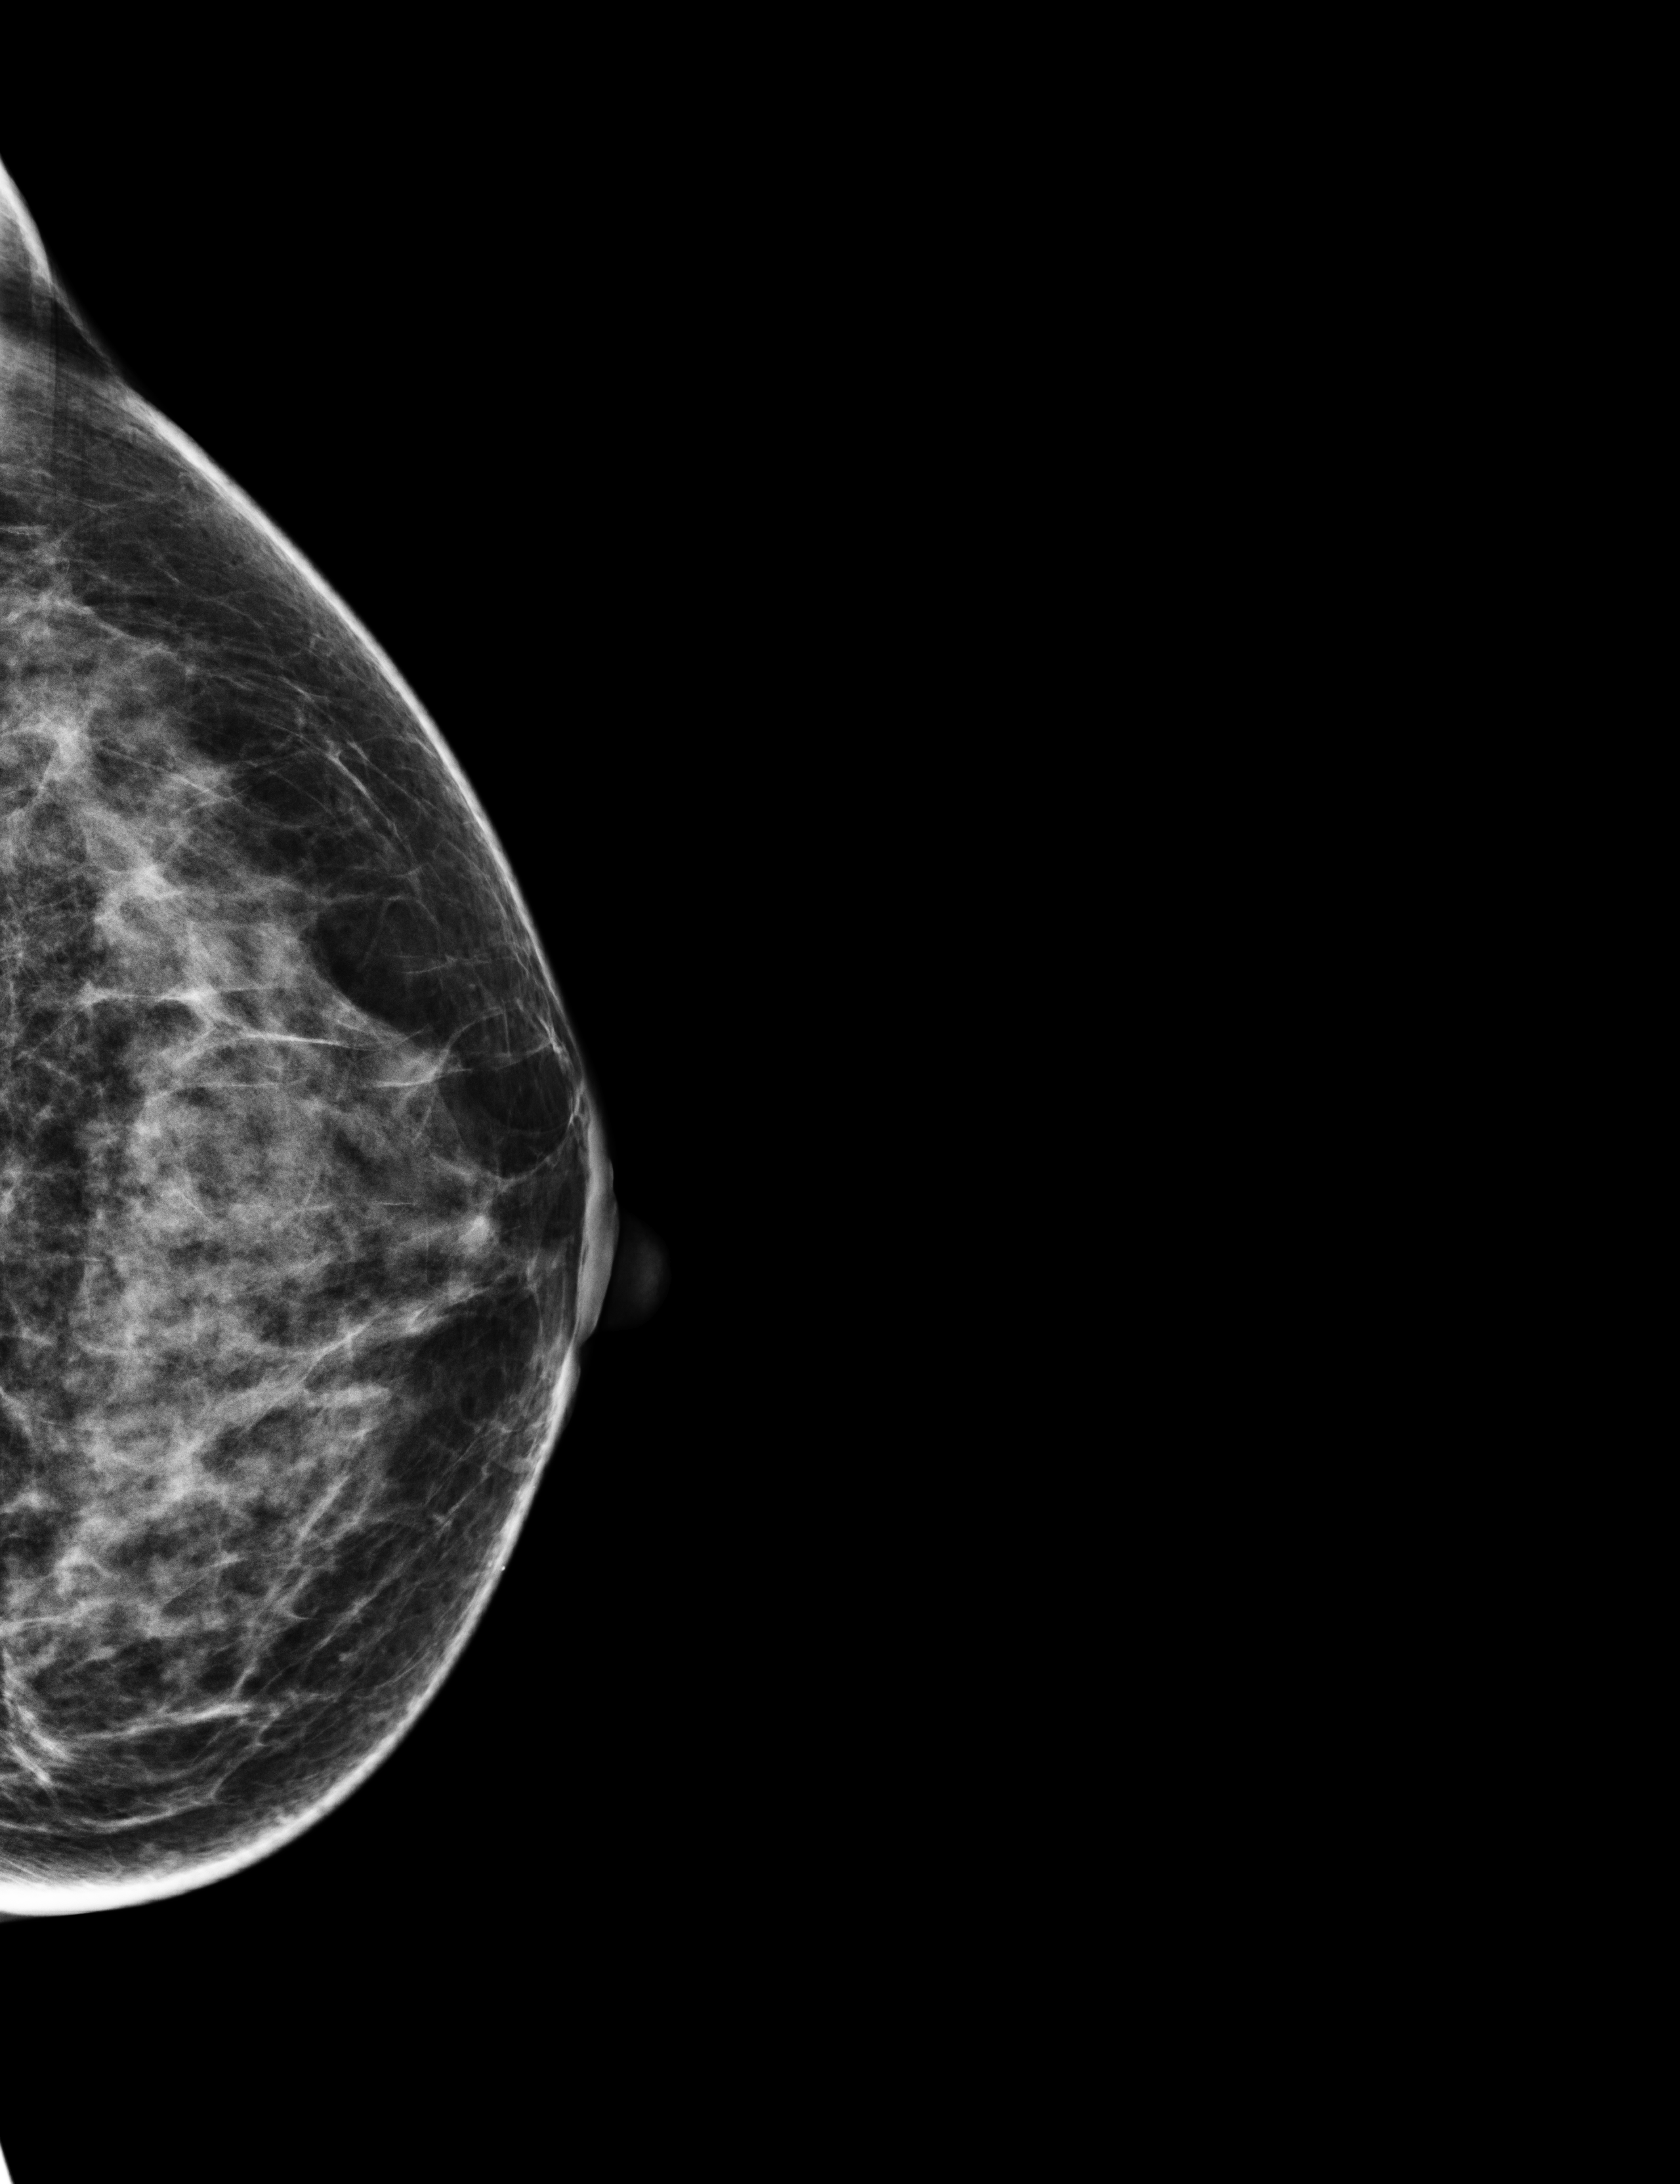
Annual screening mammography examination, compressed breast thickness 58 mm. Patient aged 55 years (female).
Image type: full-field digital mammogram. Breast: left. Projection: craniocaudal (CC) view.